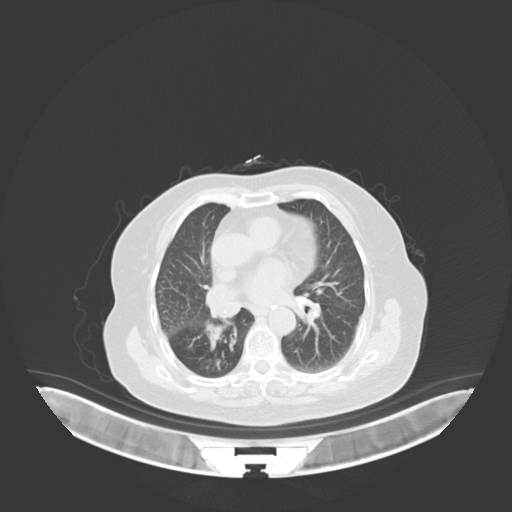
Chest CT, one axial slice. Position 28 of 76 along the scan axis. Lung window (W 1500 / L -600 HU). 3 mm slice thickness. 512 × 512 image matrix, field of view 500 × 500 mm. Female patient, age 75 years. From the clinical record (not read from this slice): clinical TNM (as recorded): T1b N0 M1a; histopathological grade: G1.
Annotated regions visible in this slice (rectangle marked by the reading radiologist):
- lung tumour (recorded histology: squamous cell carcinoma): bounding box [x1, y1, x2, y2] px = [205, 318, 226, 353]